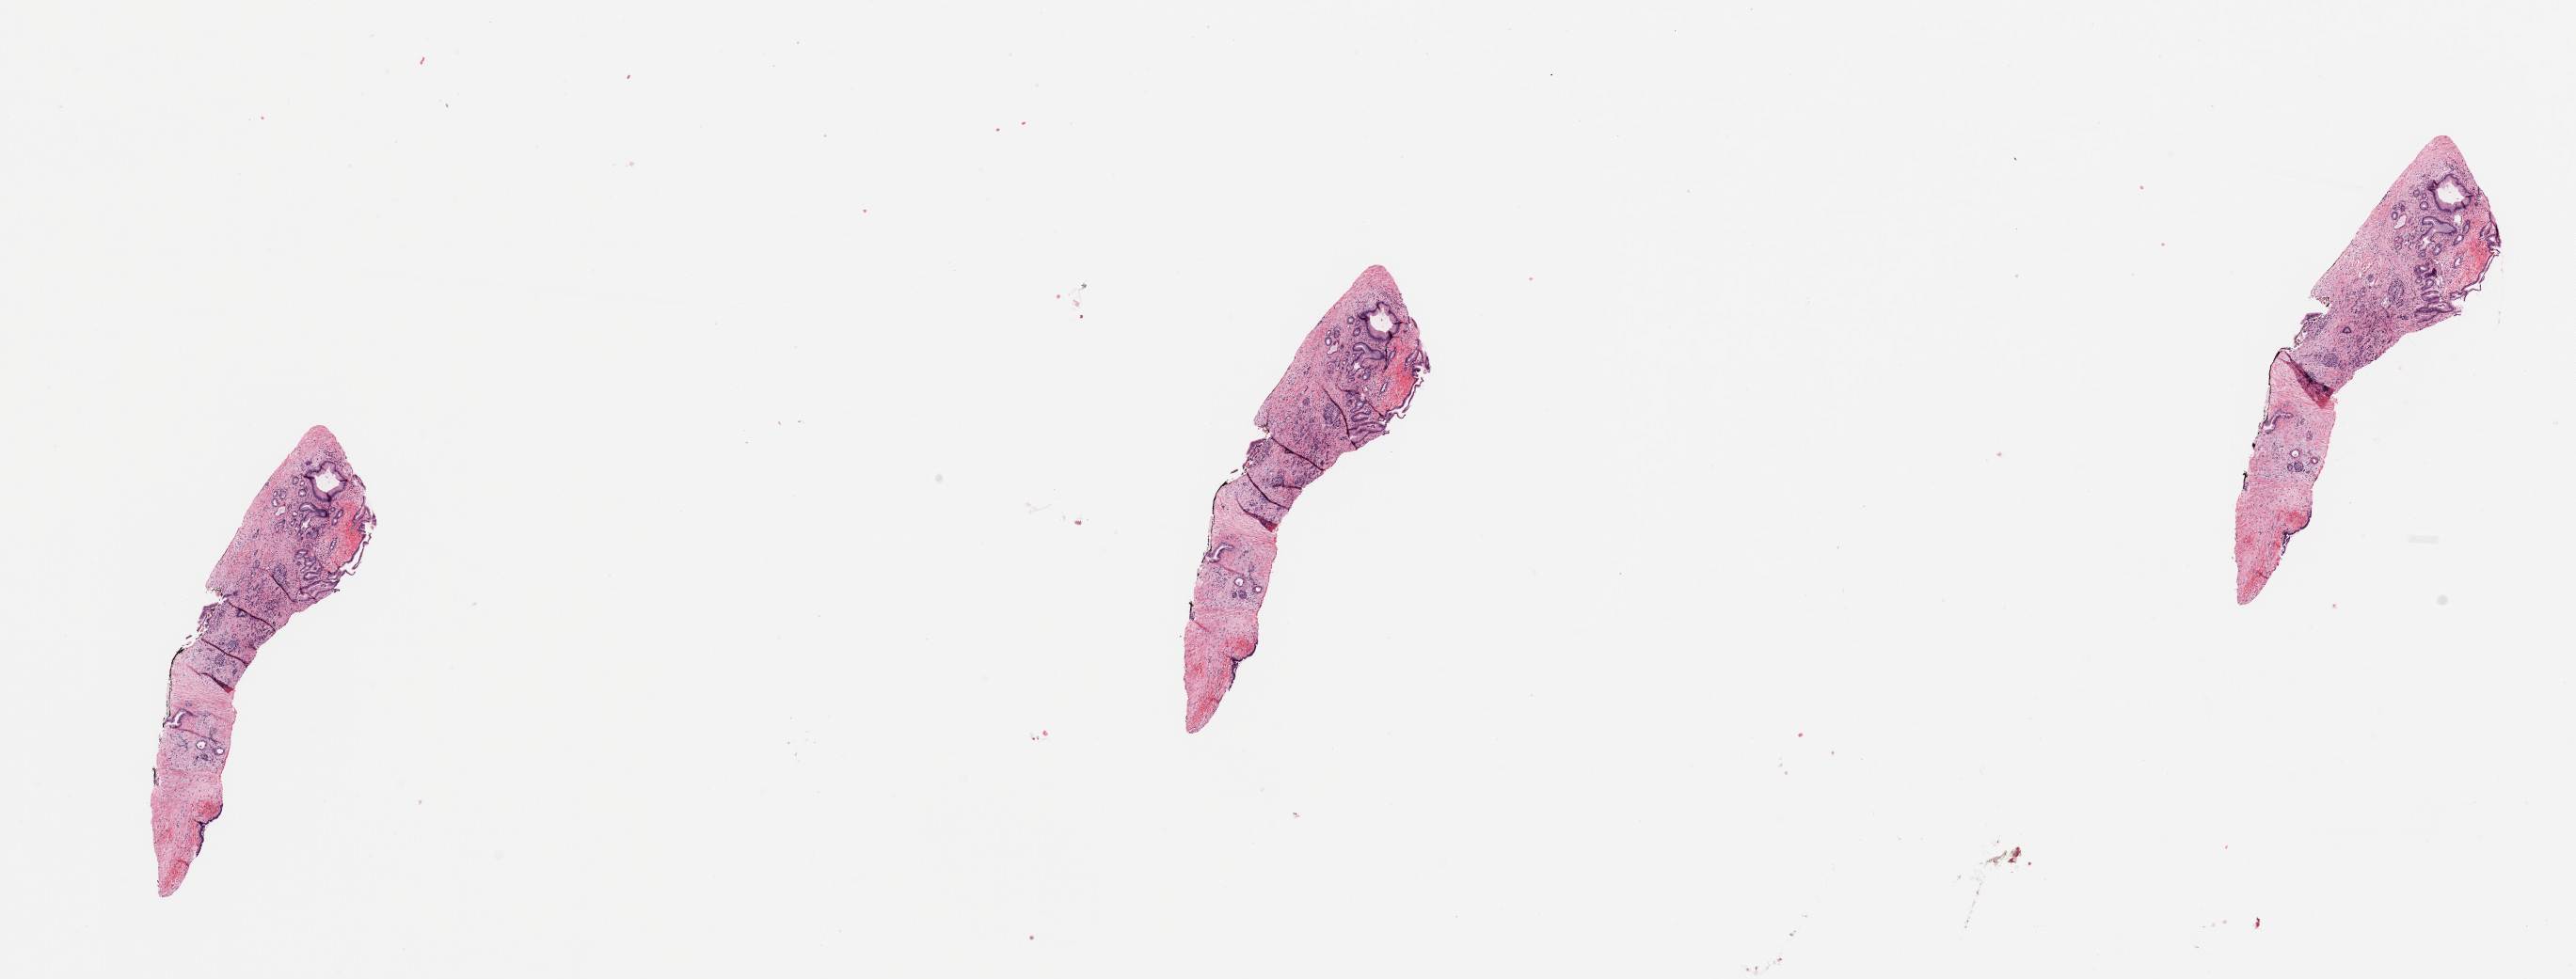
Whole-slide histology image, H&E-stained, a low-resolution overview of the entire scanned area, about 21.7 x 8.2 mm (from a 20x scan), pancreas, tumour tissue. Male, 75 y/o.
Patient diagnosis (cohort enrolment): ductal adenocarcinoma (pancreas).